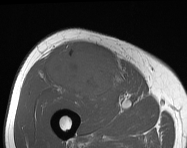
MRI of an extremity soft-tissue mass, one axial slice. Position 76 of 114 along the scan axis. MR volume resampled by the dataset authors to the PET/CT grid (not the native acquisition matrix). 3.27 mm slice thickness. 187 × 148 image matrix. Male patient. From the clinical record (not read from this slice): histological type: pleiomorphic leiomyosarcoma; grade: intermediate; site of the primary tumour: right thigh.
Structures marked on this image (expert contour drawn on MRI and transferred to this co-registered scan by the dataset authors):
- gross tumour volume including surrounding oedema: bounding box [x1, y1, x2, y2] px = [48, 45, 119, 98]
- gross tumour volume (mass): [48, 45, 119, 98]